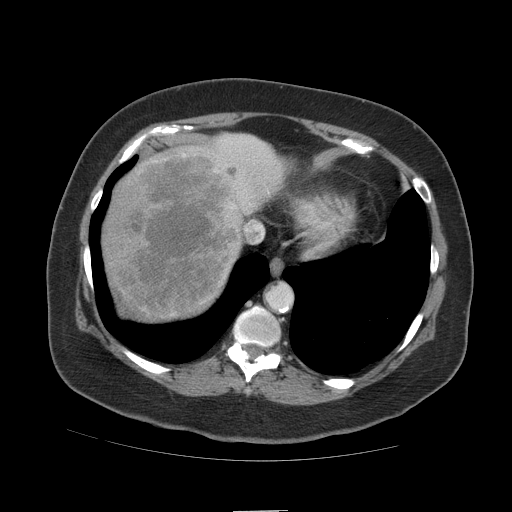
Contrast-enhanced abdominal CT (liver protocol), one axial slice. Slice 92 of 109 in the series (ordered by position). 140 kVp. Soft-tissue window (W 400 / L 40 HU). 2.5 mm slice thickness. 512 × 512 image matrix, field of view 420 × 420 mm. Case-level facts recorded for this patient, not image findings: diagnosis: hepatocellular carcinoma (patient treated with transarterial chemoembolisation; whether this scan precedes or follows treatment is not stated here); TNM stage (as recorded): Stage-IVB; Child-Pugh class: A; tumour differentiation: poorly differentiated; tumour nodularity: multinodular.
Structures marked on this image (semi-automatic segmentation, software-assisted and operator-edited):
- liver parenchyma outside the tumour (the mass and vessels are separate outlines, so this box may not span the whole liver): bounding box (x1, y1, x2, y2) in pixels: (102, 134, 284, 320)
- mass: (102, 146, 247, 317)
- liver vessels: (225, 140, 251, 144)